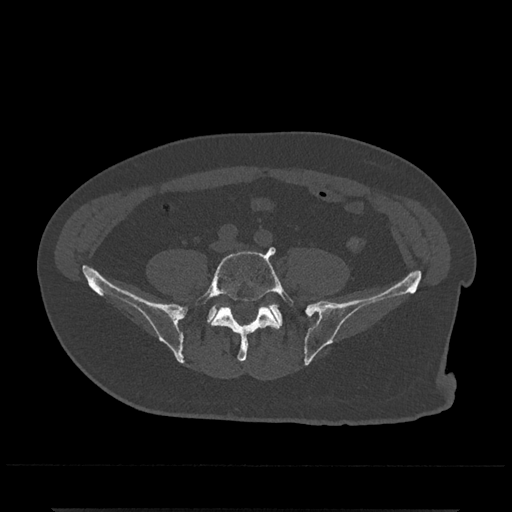
CT including the spine, one axial slice. Slice 79 of 797 in the series (ordered by position). 120 kVp. Bone window (W 1800 / L 400 HU). 512 × 512 image matrix, field of view 393 × 393 mm. Male patient, age 67 years. Case-level facts recorded for this patient, not image findings: primary cancer: prostate.
Structures marked on this image (semi-automatically segmented with operator editing):
- L5 vertebra: box from (x=196, y=247) to (x=294, y=362) px